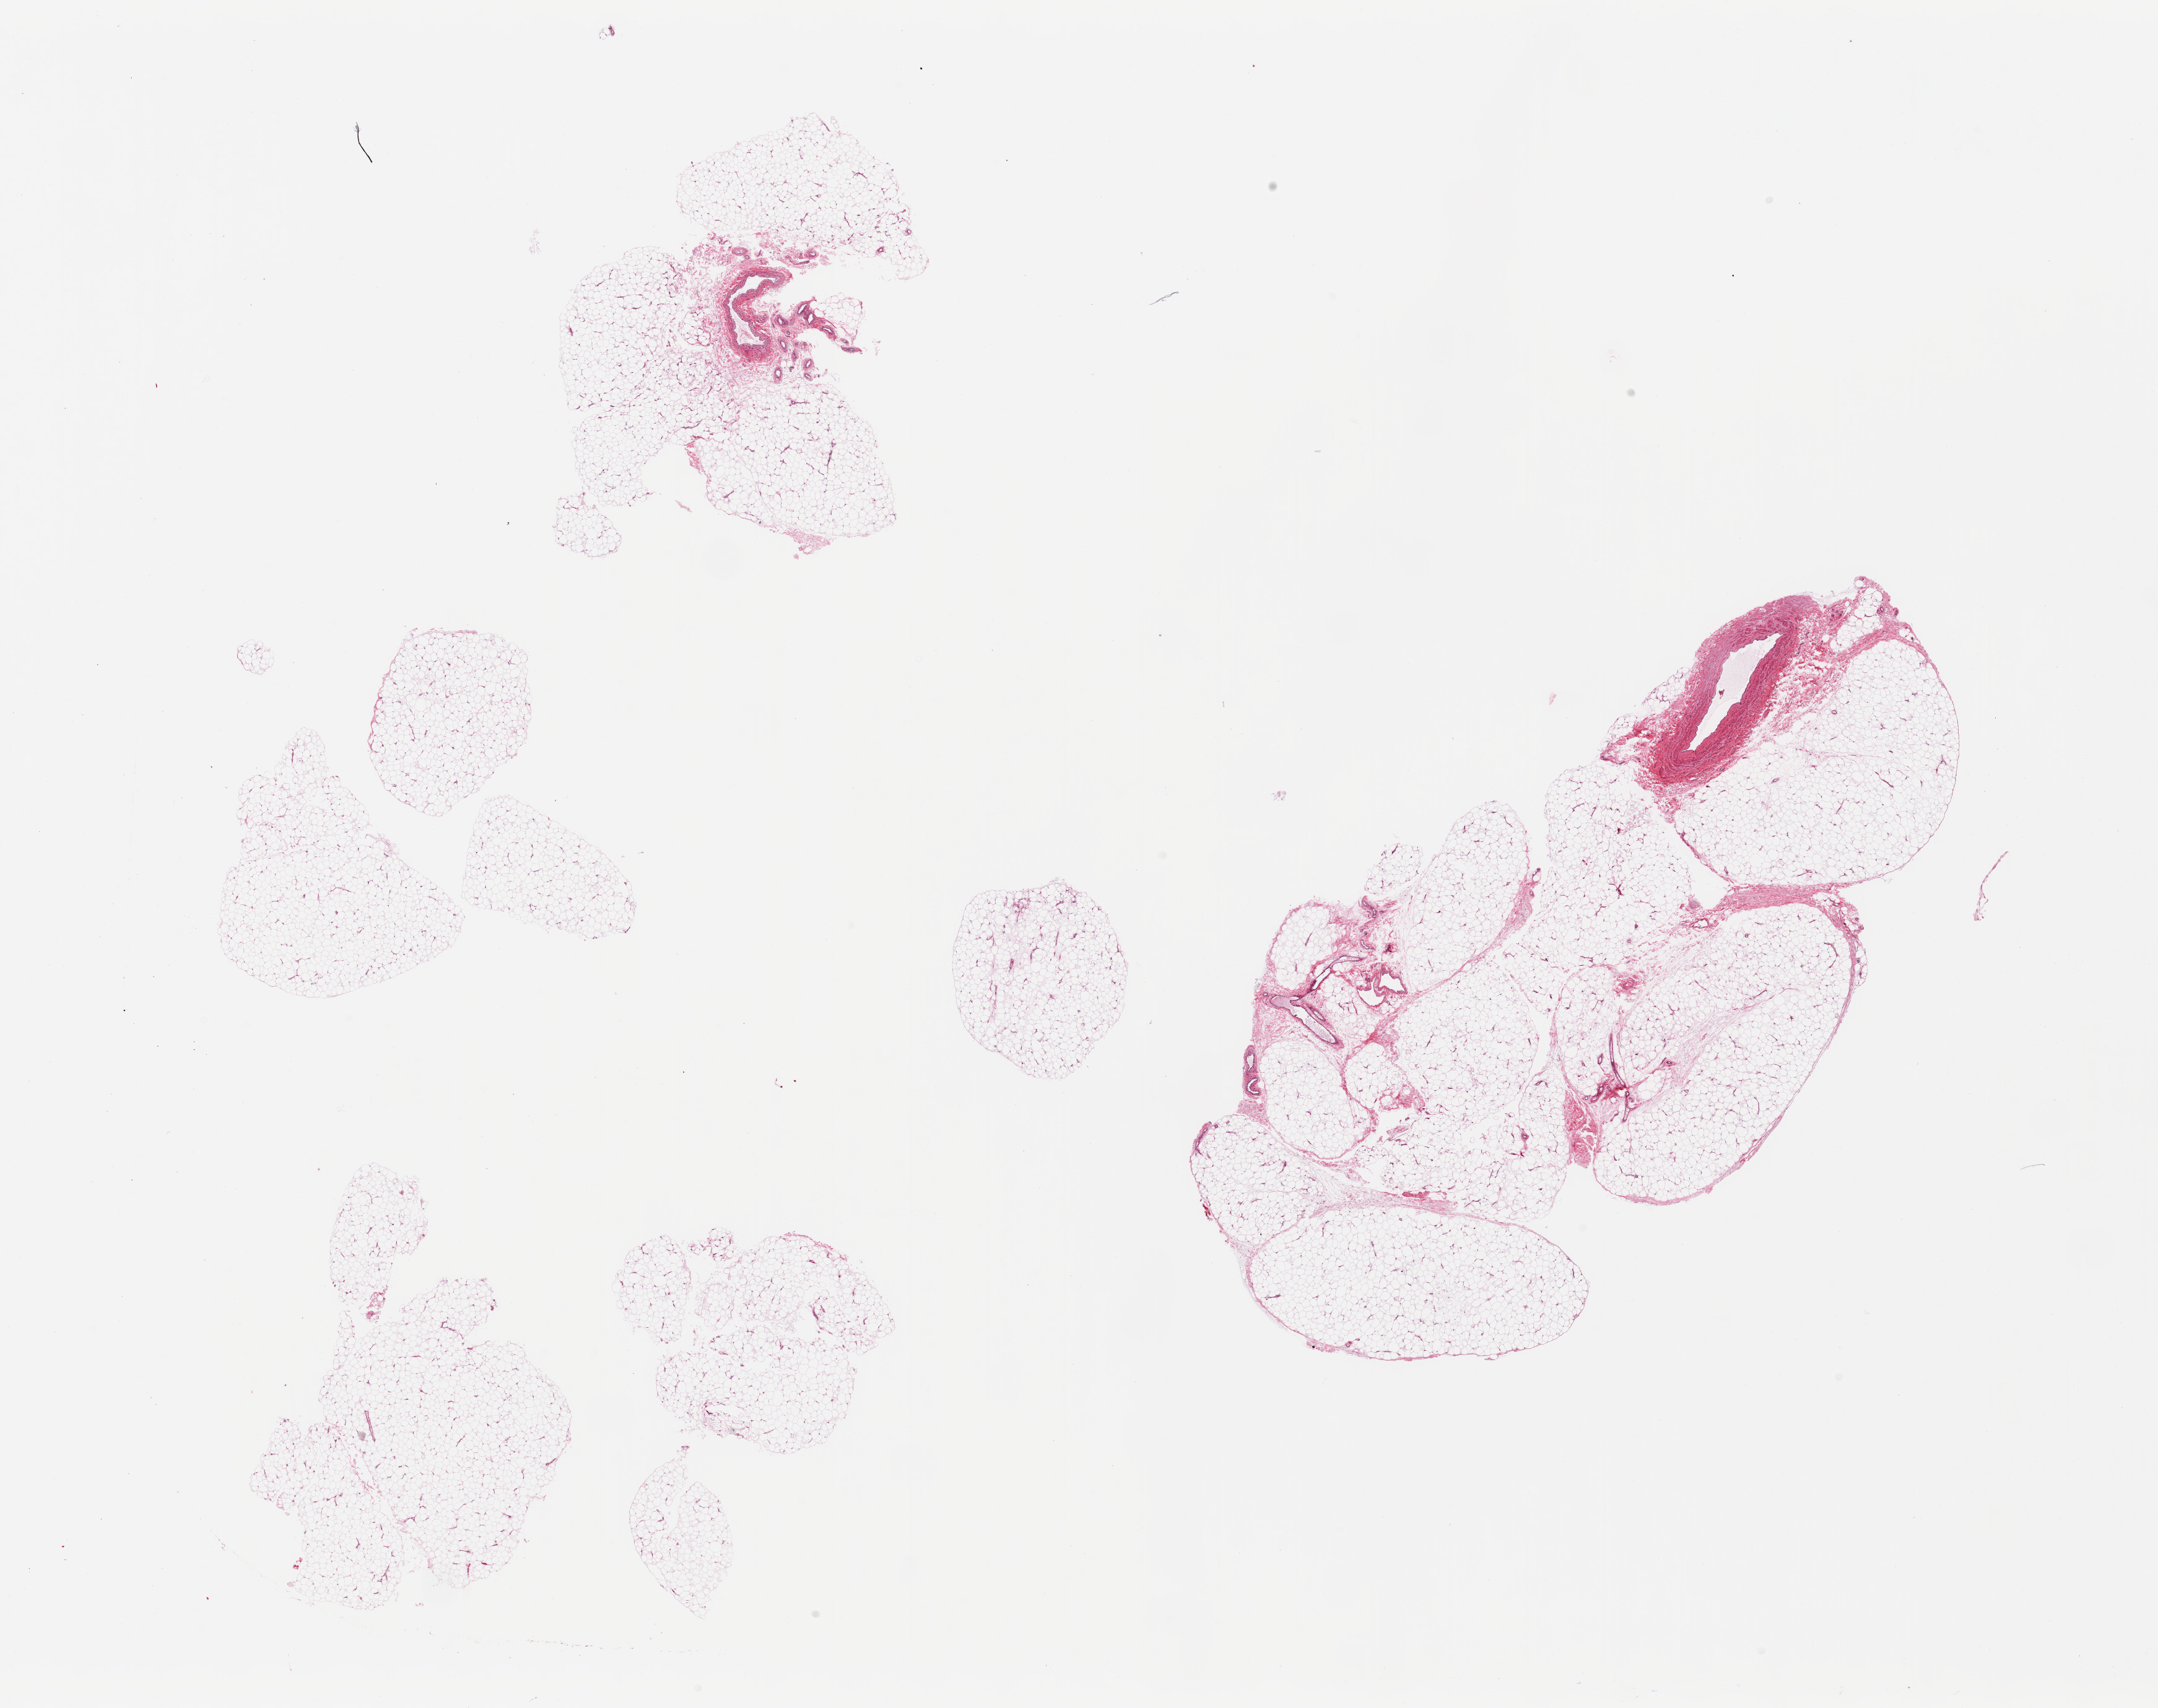
Digitized H&E-stained section — a low-resolution overview of the entire scanned area, about 27.6 x 21.8 mm (from a 20x scan). PAXgene-fixed paraffin-embedded (PFPE) section. Section of adipose tissue (target tissue). Donor tissue sample. Donor: female.
Pathologist's review note for this sample: 3 pieces (fragemented), ~10% fascia/vascular elements.